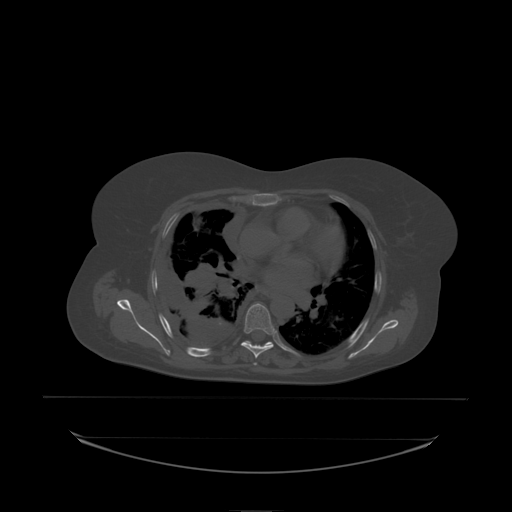
CT including the spine, one axial slice. Slice 149 of 242 in the series (ordered by position). Bone window (W 1800 / L 400 HU). 2.5 mm slice thickness. 512 × 512 image matrix, field of view 500 × 500 mm. Patient: female, 53 years. From the clinical record (not read from this slice): primary cancer: lung.
Structures marked on this image (semi-automatic segmentation, software-assisted and operator-edited):
- T6 vertebra: box from (x=245, y=304) to (x=276, y=335) px